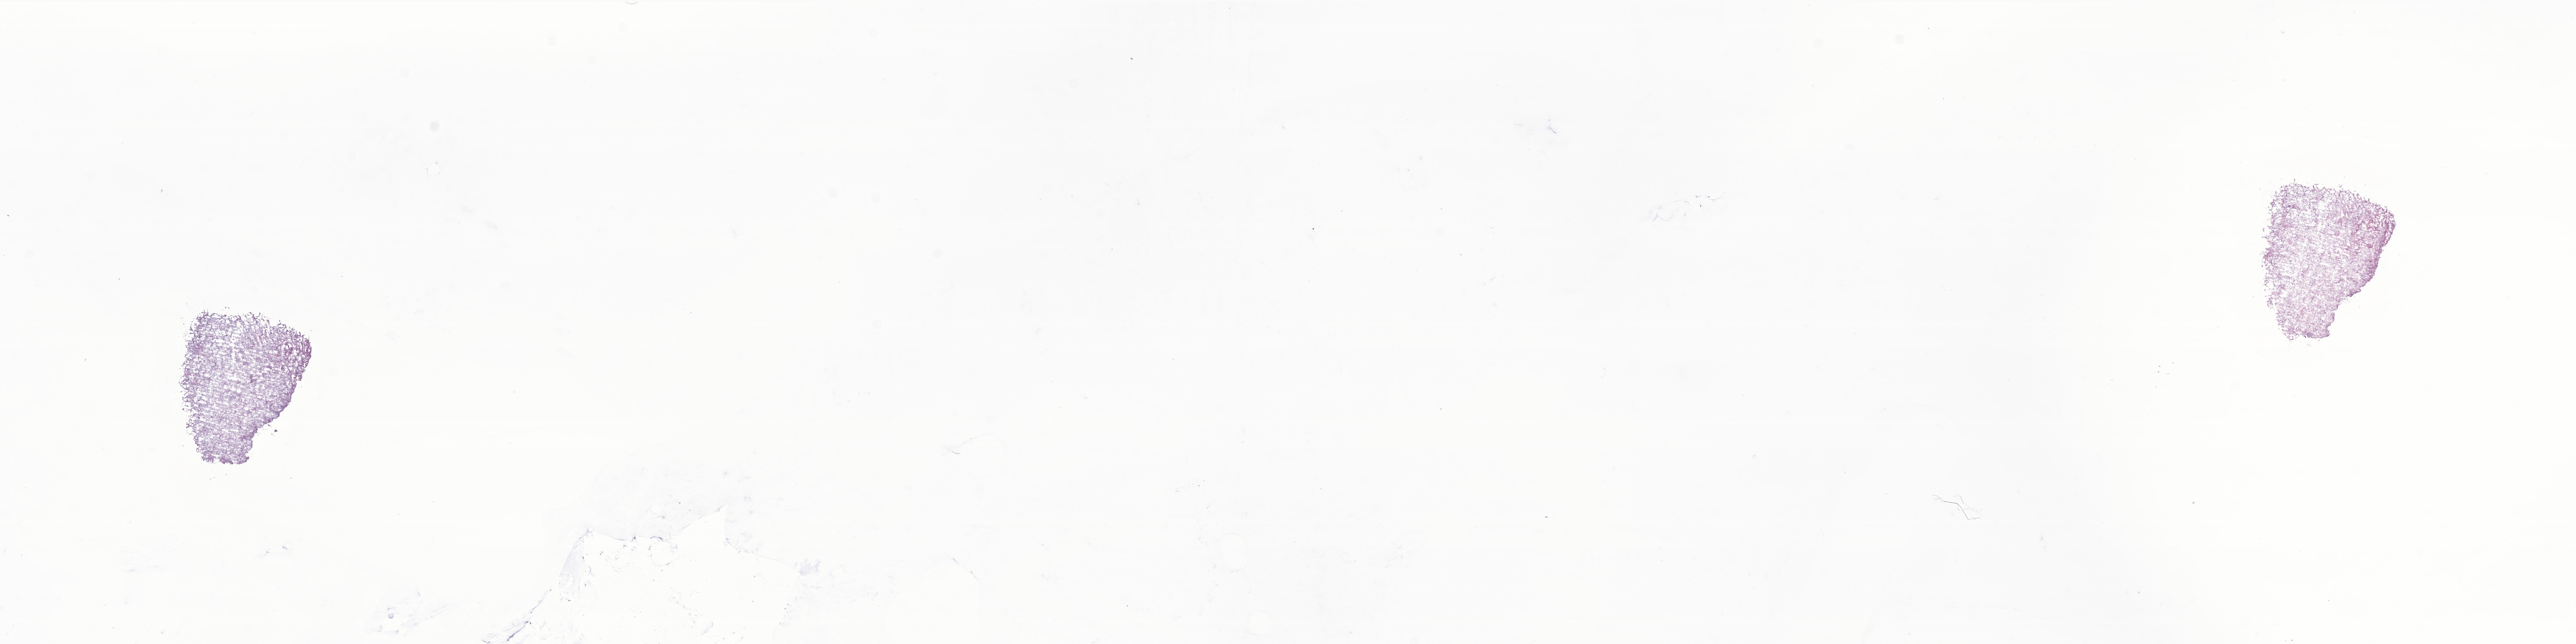
Digitized haematoxylin and eosin-stained section of tumor tissue from the brain stem, whole scanned area (about 27.7 x 6.9 mm) shown as a low-resolution overview; frozen section. Patient female; age 52 months (4 years 4 months).
Diagnosis (ICD-O-3 morphology term): Pilocytic astrocytoma.